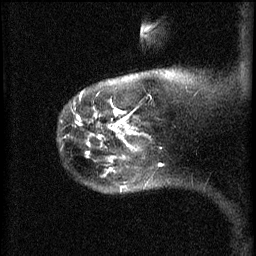
Breast MRI (dynamic contrast-enhanced), one sagittal slice. Position 53 of 60 along the scan axis. 3 images stored at this slice position (order not interpretable as contrast timing). 1.5 T. TE 4.2 ms, TR 11 ms. 256 × 256 image matrix, field of view 180 × 180 mm. Patient: female, 44 years.
Structures marked on this image (semi-automatic segmentation, software-assisted and operator-edited):
- analysis volume of interest (the breast-tissue region the enhancement analysis was run in; not a lesion): bounding box [x1, y1, x2, y2] px = [112, 124, 149, 169]
- tumour enhancement mask (voxels above the 70 % enhancement threshold inside the analysis volume of interest): [116, 124, 137, 139]